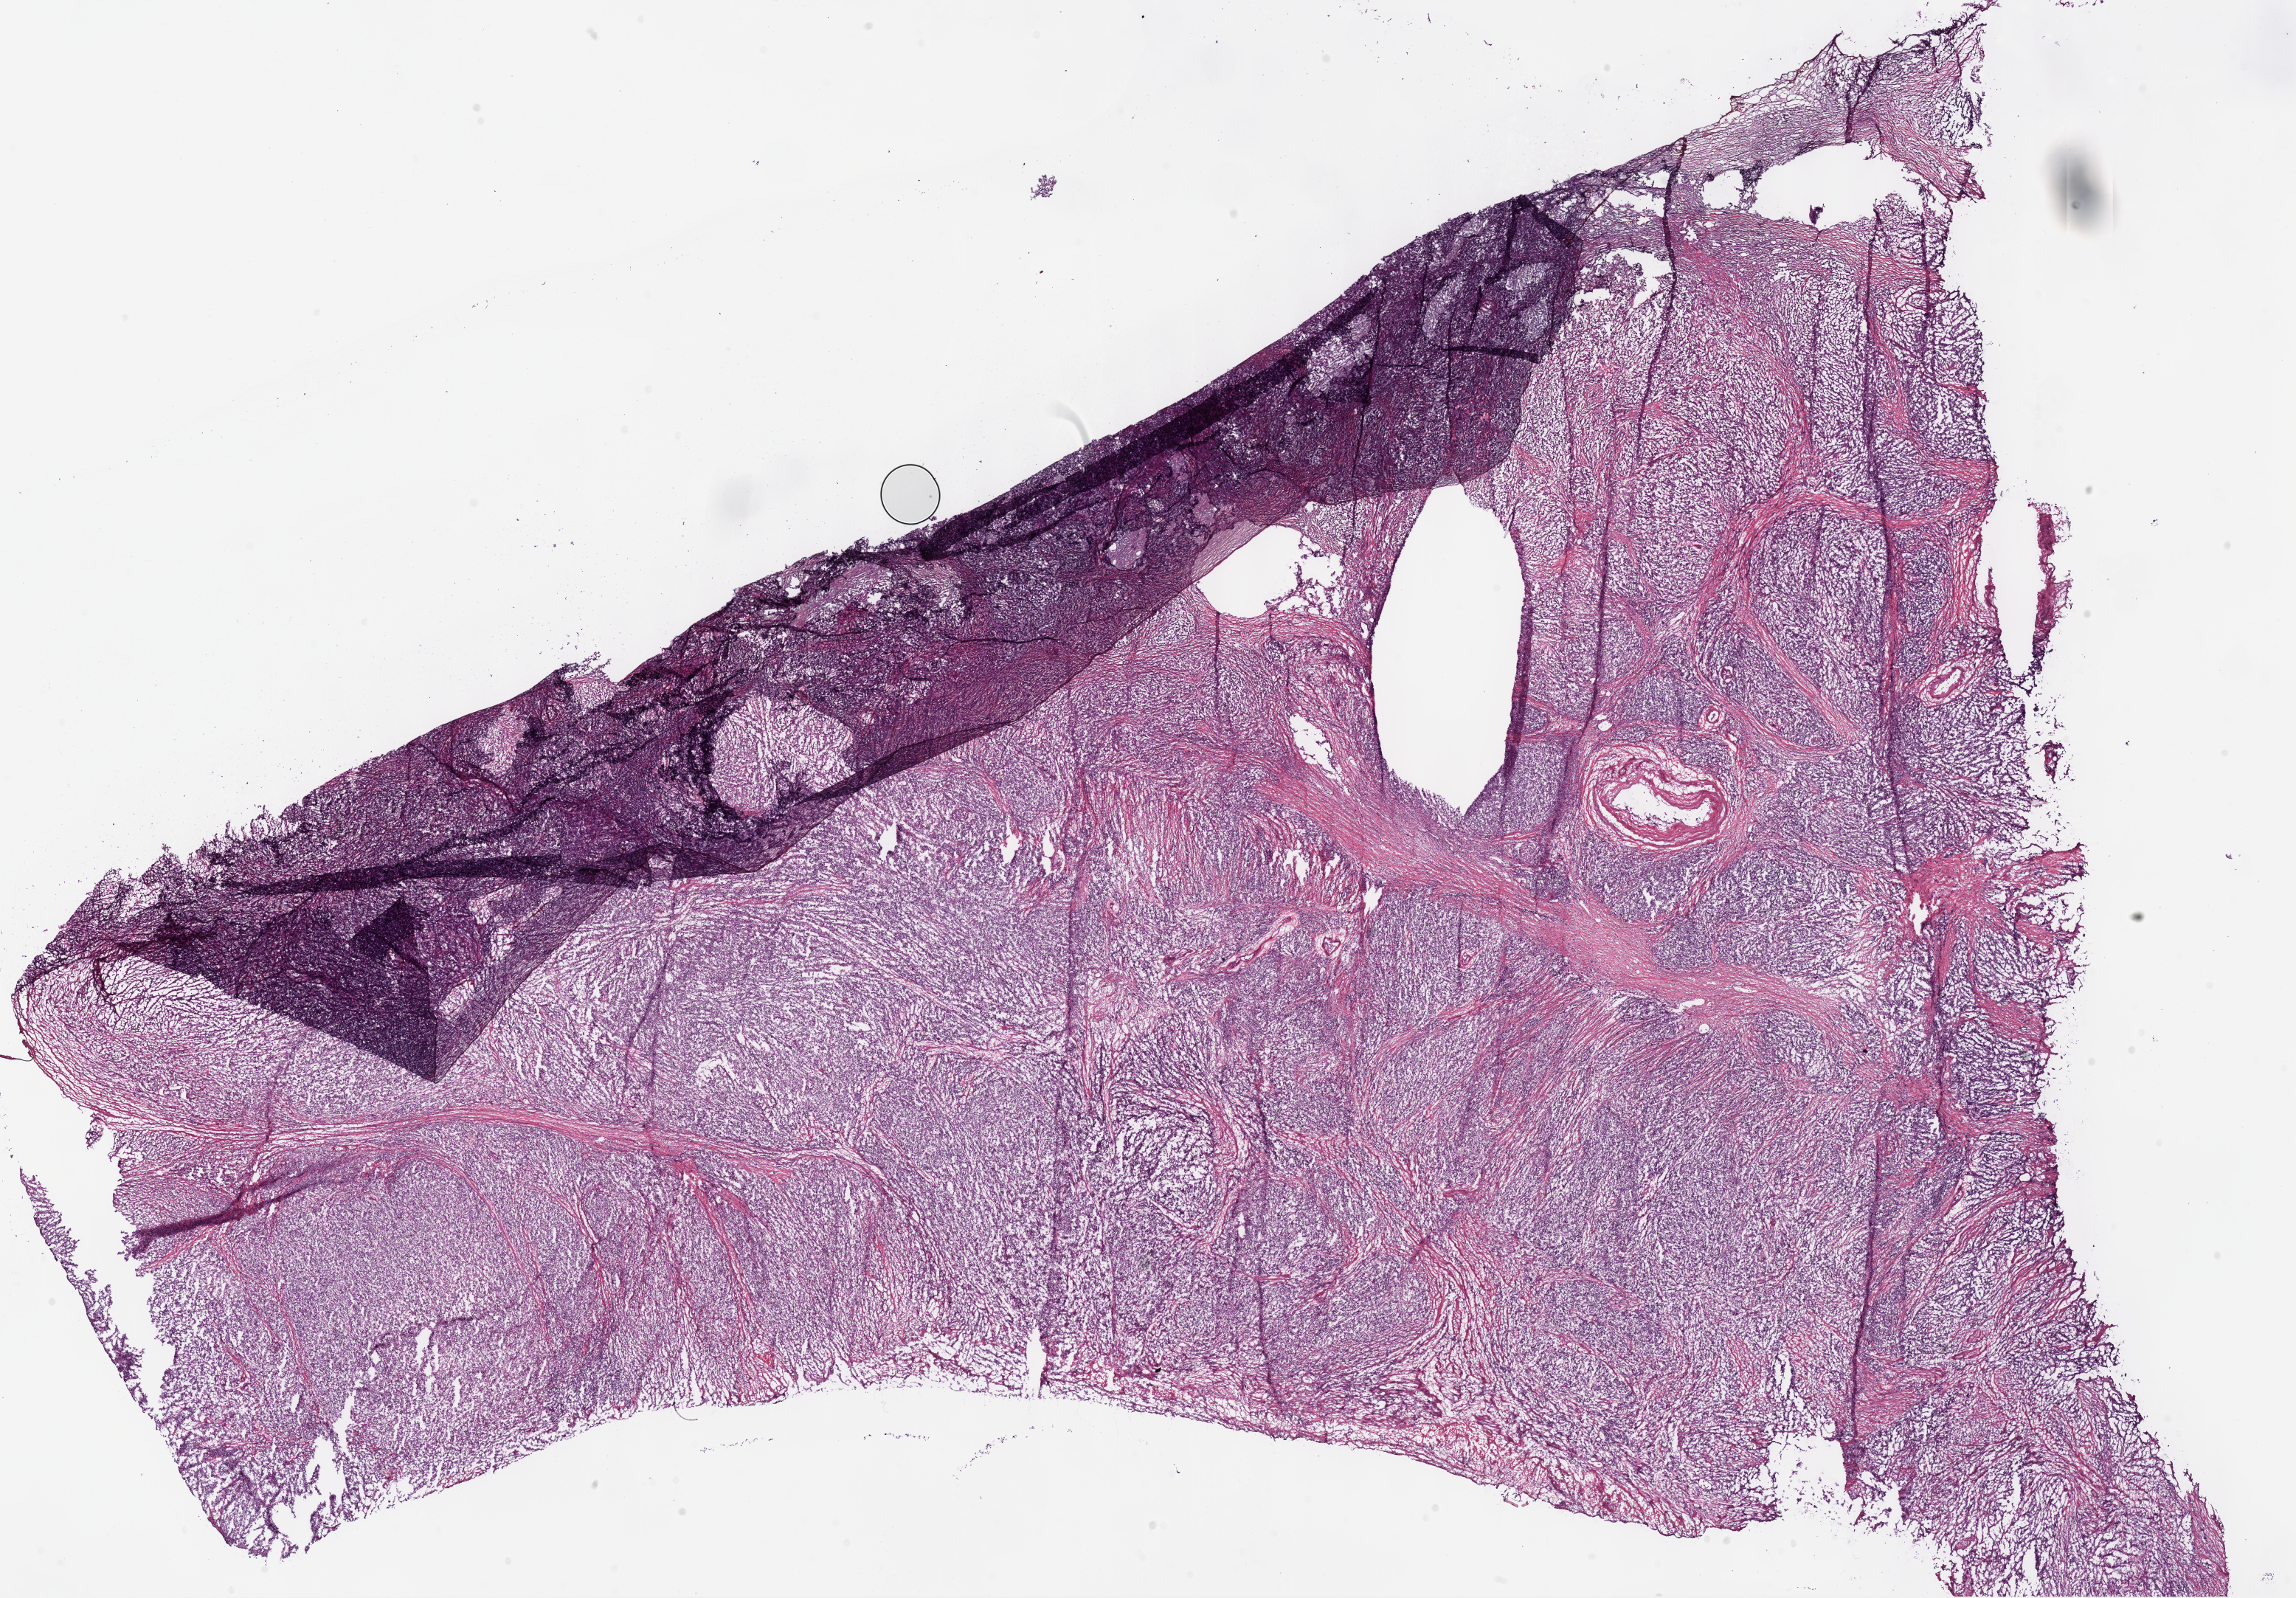
H&E whole-slide image — whole scanned area (about 24.5 x 17.0 mm, slide scanned at 40x) shown as a low-resolution overview. Frozen section from the bottom of the tissue portion. Sample: primary tumour, stomach. Patient: female, age at initial diagnosis 57 years. Histologic grade: G3 (poorly differentiated). Slide review estimates, as recorded: tumour cells 90%, tumour nuclei 80%, normal cells 0%, stromal cells 10%, necrosis 0%.
* AJCC pathologic stage: IIIC (7th edition)
* lymph nodes positive (case pathology): 11 of 11 examined
* histologic diagnosis: Adenocarcinoma, intestinal type (gastric antrum)